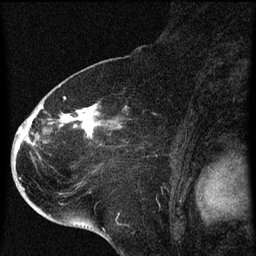
Breast MRI (dynamic contrast-enhanced), one sagittal slice; slice 35 of 60 in the series (ordered by position); dynamic contrast-enhanced series, image 2 of 4 at this slice position (ordered by acquisition); 1.5 T; TE 4.2 ms, TR 8 ms; 2 mm slice thickness; 256 × 256 image matrix. Female patient, age 71 years.
Structures marked on this image (semi-automatically segmented with operator editing):
- analysis volume of interest (the breast-tissue region the enhancement analysis was run in; not a lesion): bounding box <32,86,140,205> (left, top, right, bottom; pixels)
- tumour enhancement mask (voxels above the 70 % enhancement threshold inside the analysis volume of interest): <41,96,97,139>